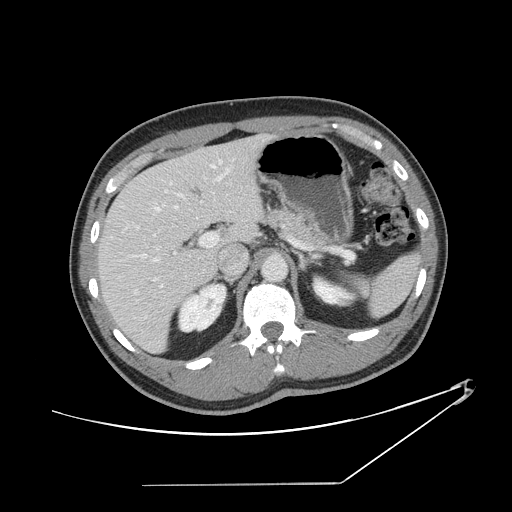
Contrast-enhanced abdominal CT, one axial slice; position 87 of 152 along the scan axis; reconstruction kernel STANDARD; intravenous contrast given; soft-tissue window (W 400 / L 40 HU); 2.5 mm slice thickness; 512 × 512 image matrix, field of view 432 × 432 mm. Male patient, age 45 years. From the clinical record (not read from this slice): diagnosis: colorectal cancer liver metastases, imaged before liver resection.
Outlined on this slice (expert manual segmentation):
- hepatic veins: bounding box <112,159,223,294> (left, top, right, bottom; pixels)
- liver: <99,136,264,351>
- planned liver remnant (the part of the liver to remain after resection): <99,156,225,351>
- portal vein (with intrahepatic branches): <137,169,306,319>